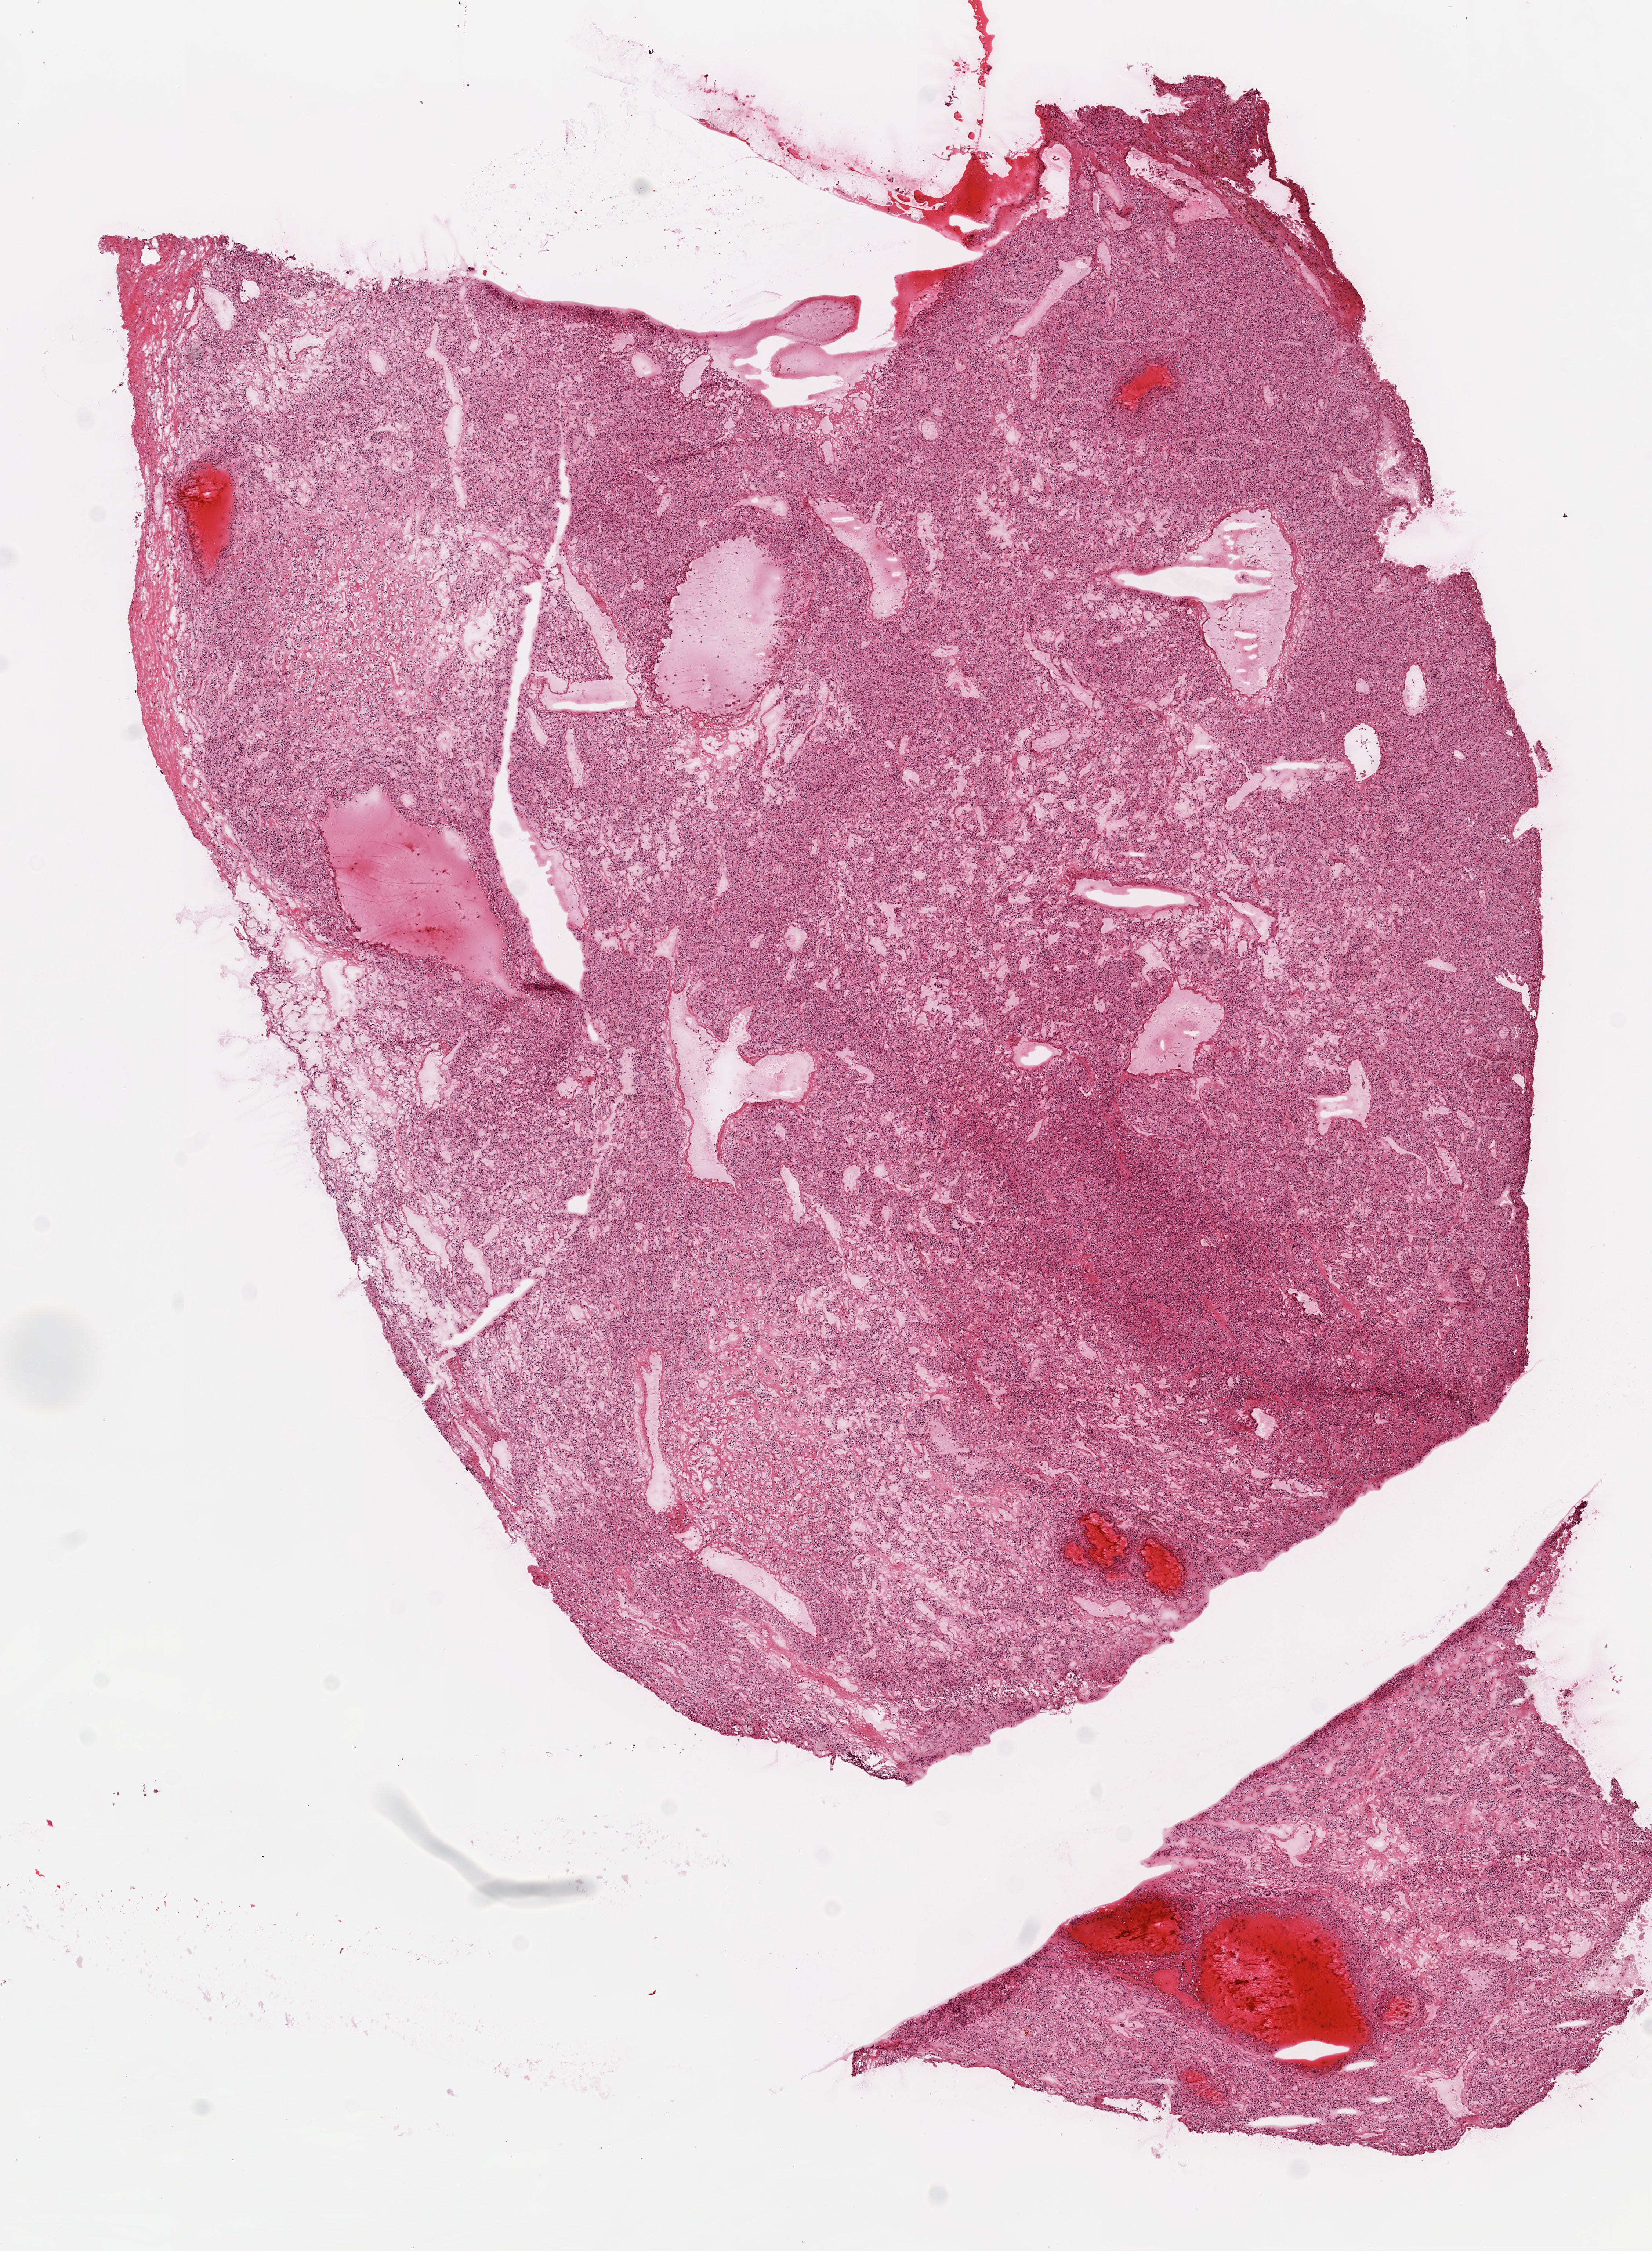
Whole-slide histology image, H&E, shown as a low-resolution overview of the whole scanned area (about 9.0 x 12.3 mm, slide scanned at 20x); frozen section from the top of the tissue portion; primary tumour sample from the kidney. Male patient; age at initial diagnosis 59 years.
Diagnosis: Clear cell adenocarcinoma, NOS.